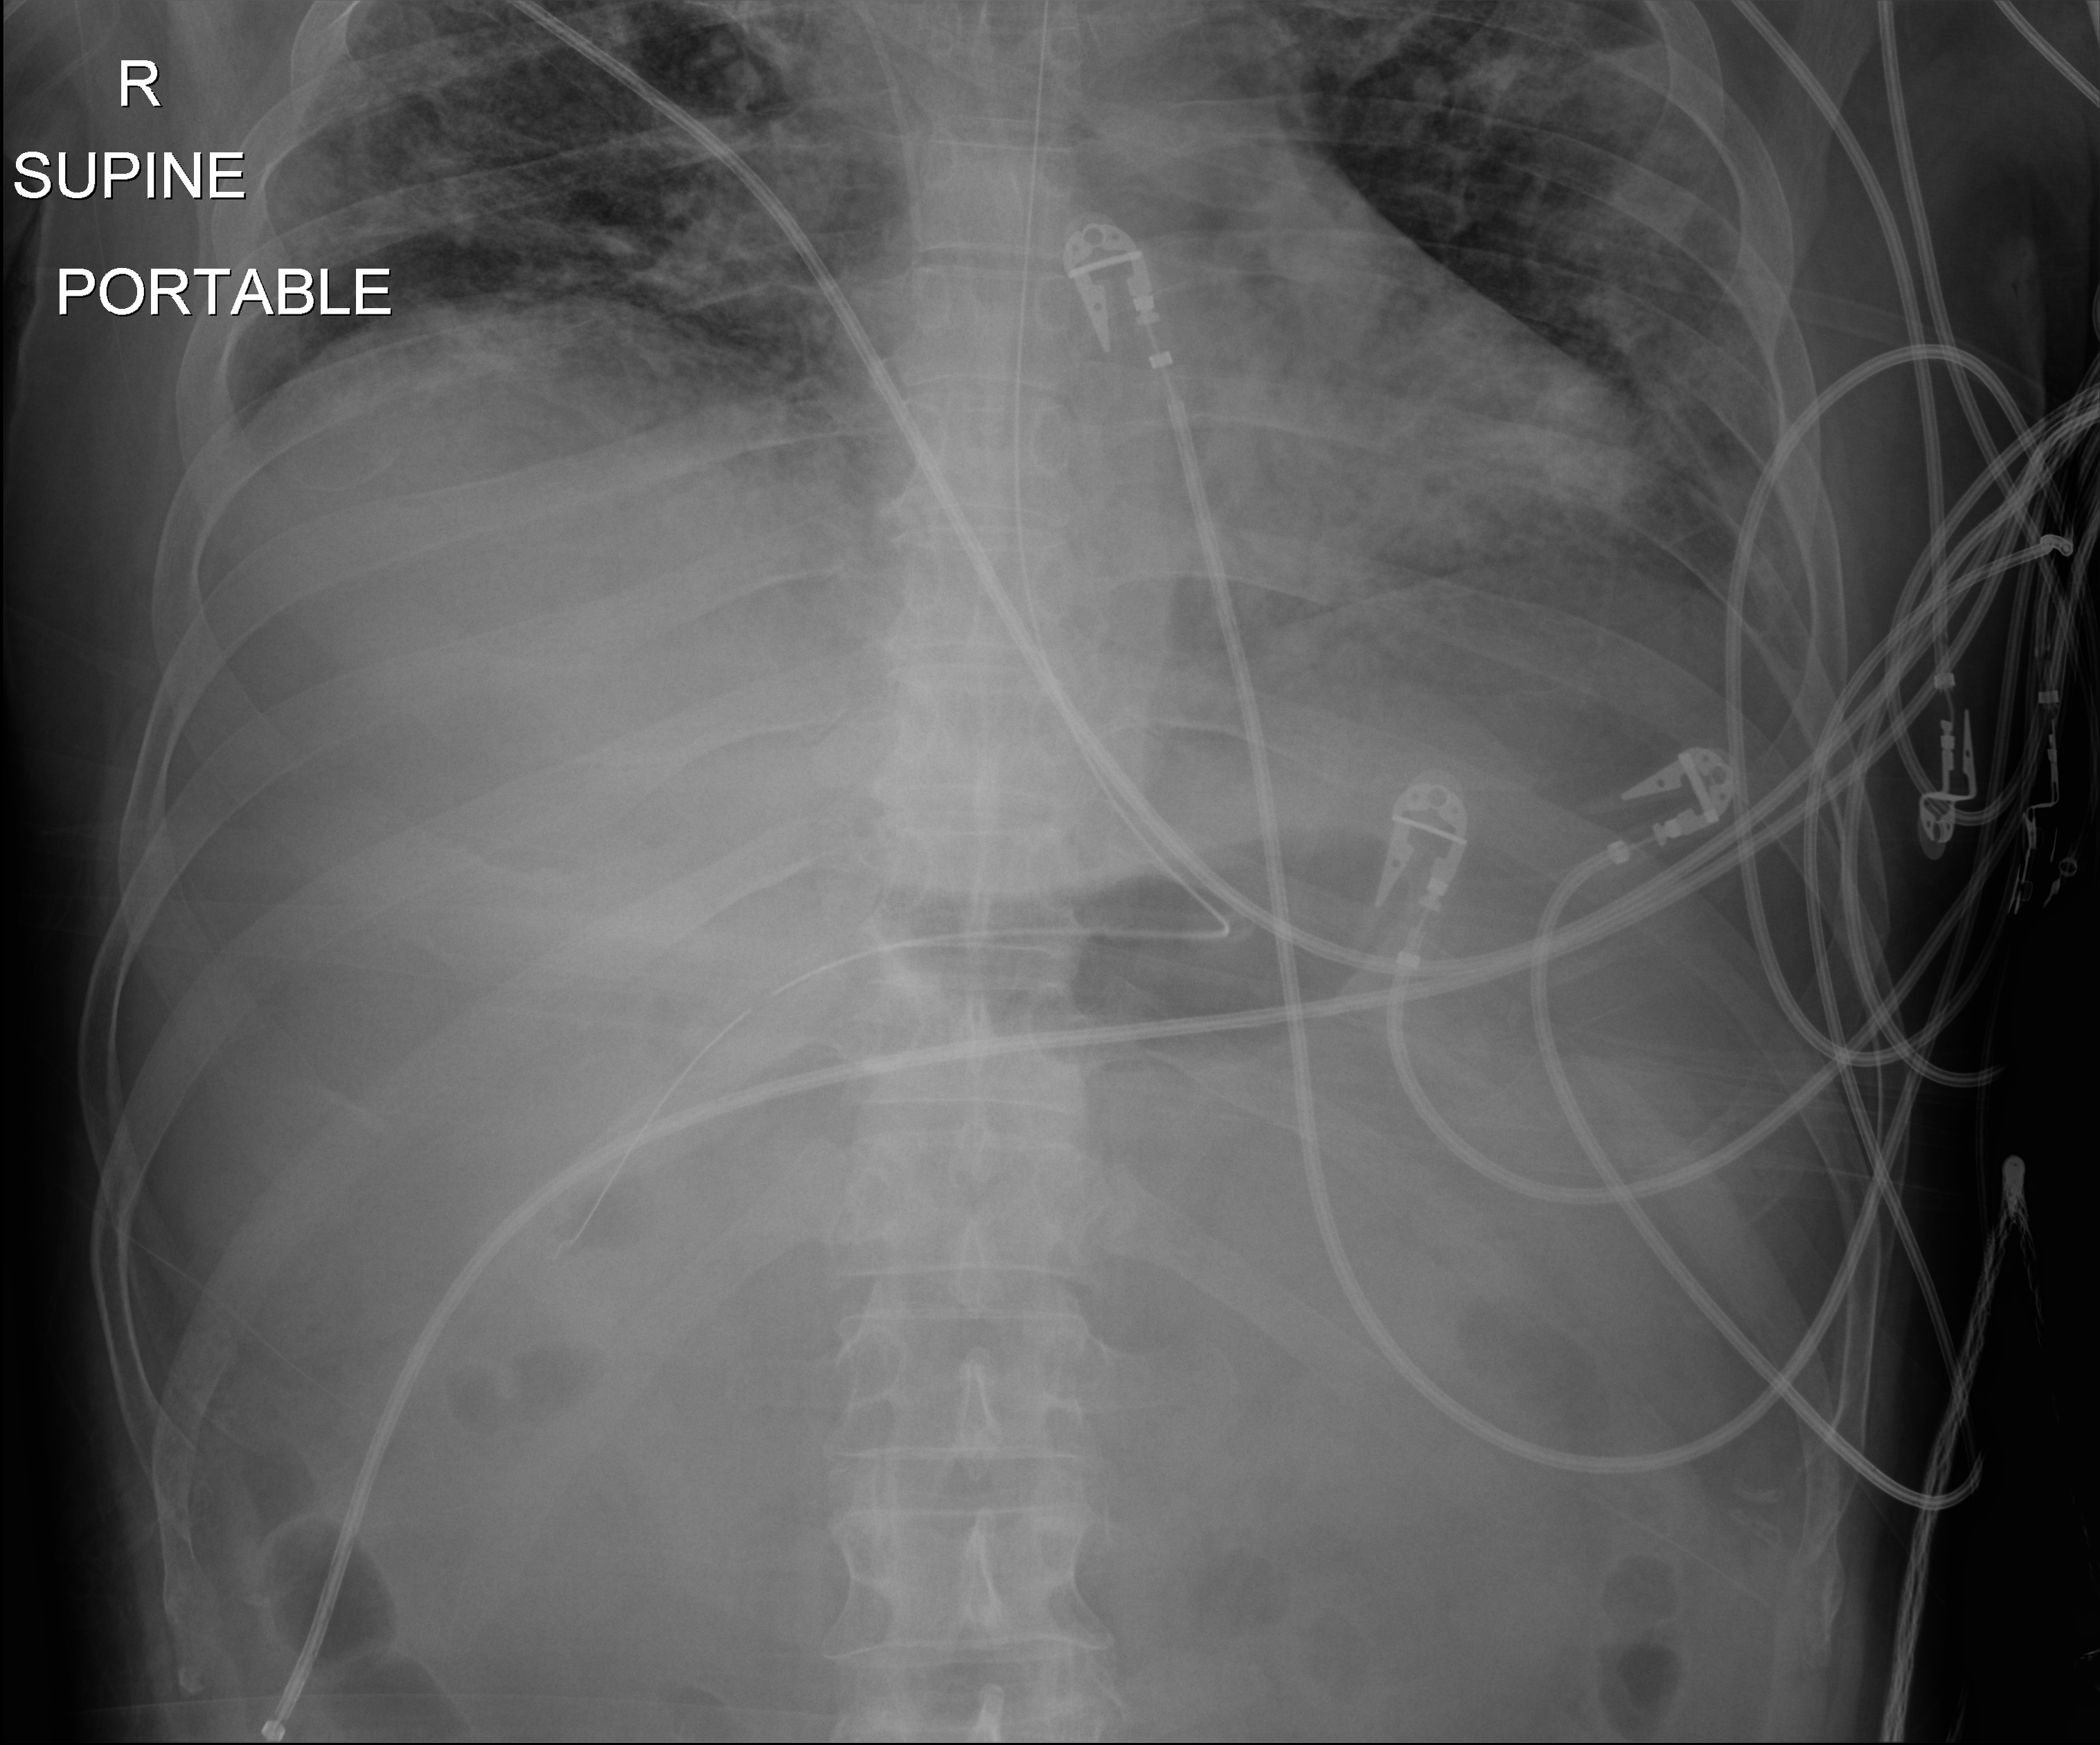
Chest X-ray (portable), anteroposterior (AP) projection. Male patient hospitalised with COVID-19, age 18–59 years.
From the hospital-stay record, not from the radiograph (when in the stay this image was taken is not recorded): admitted to intensive care during this hospital stay: yes; mechanically ventilated during this hospital stay: yes.